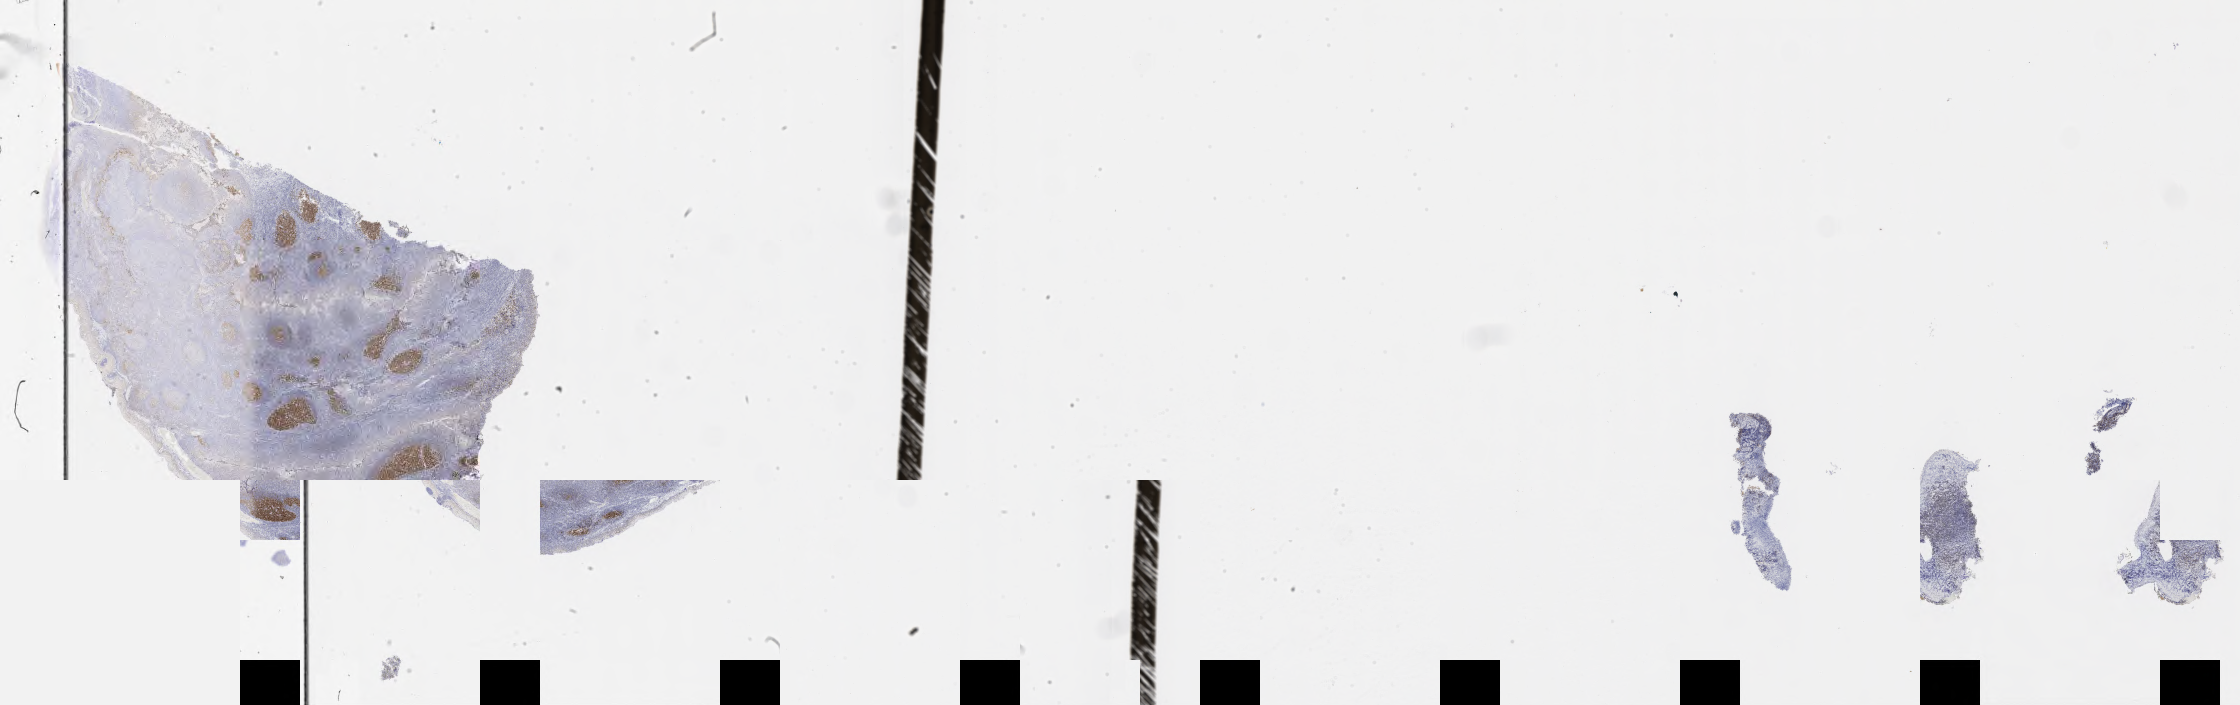
IHC for BCL6, whole-slide image, whole scanned area (about 36.2 x 11.4 mm) shown as a low-resolution overview; specimen: tumor tissue; anatomic site: colon. Patient: male, 28 years old.
* histologic diagnosis: Burkitt lymphoma, NOS